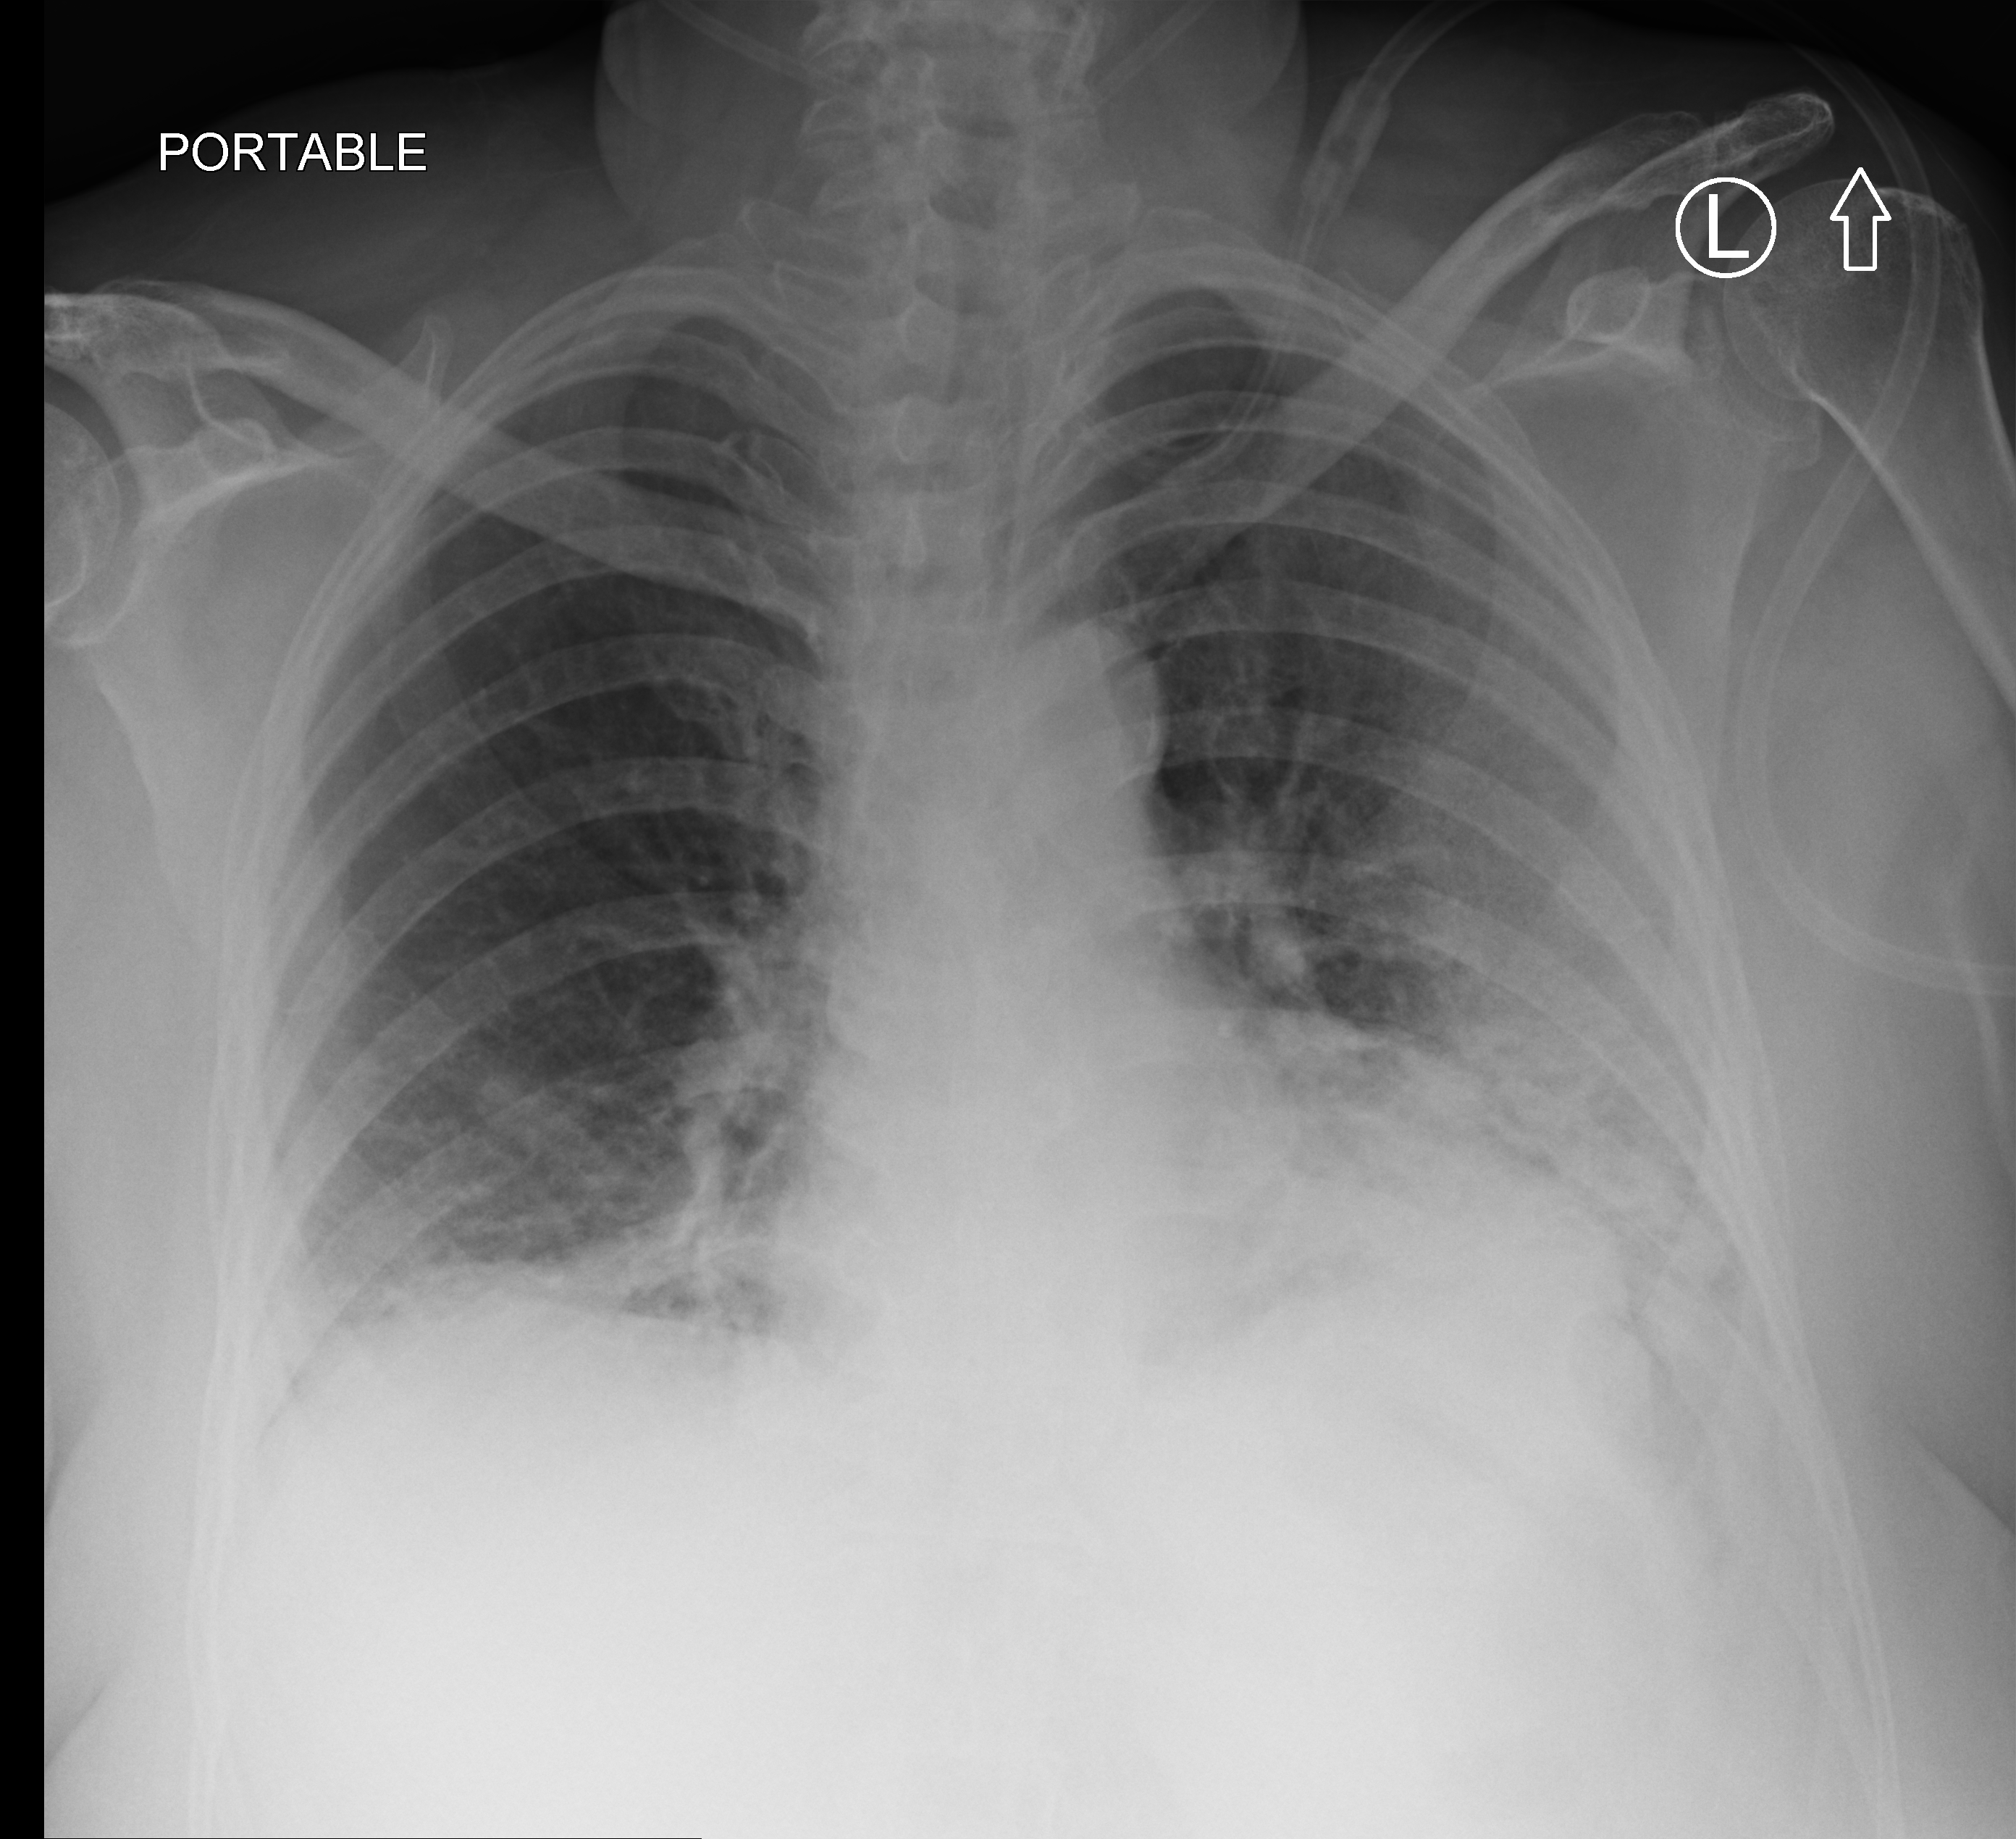
Bedside chest radiograph (computed radiography); anteroposterior (AP) projection. Female patient hospitalised with COVID-19, age 60–74 years.
Admission-level facts for this patient (not findings on this image; timing relative to this image not recorded): admitted to intensive care during this hospital stay: no; mechanically ventilated during this hospital stay: no; length of hospital stay: 18 days.